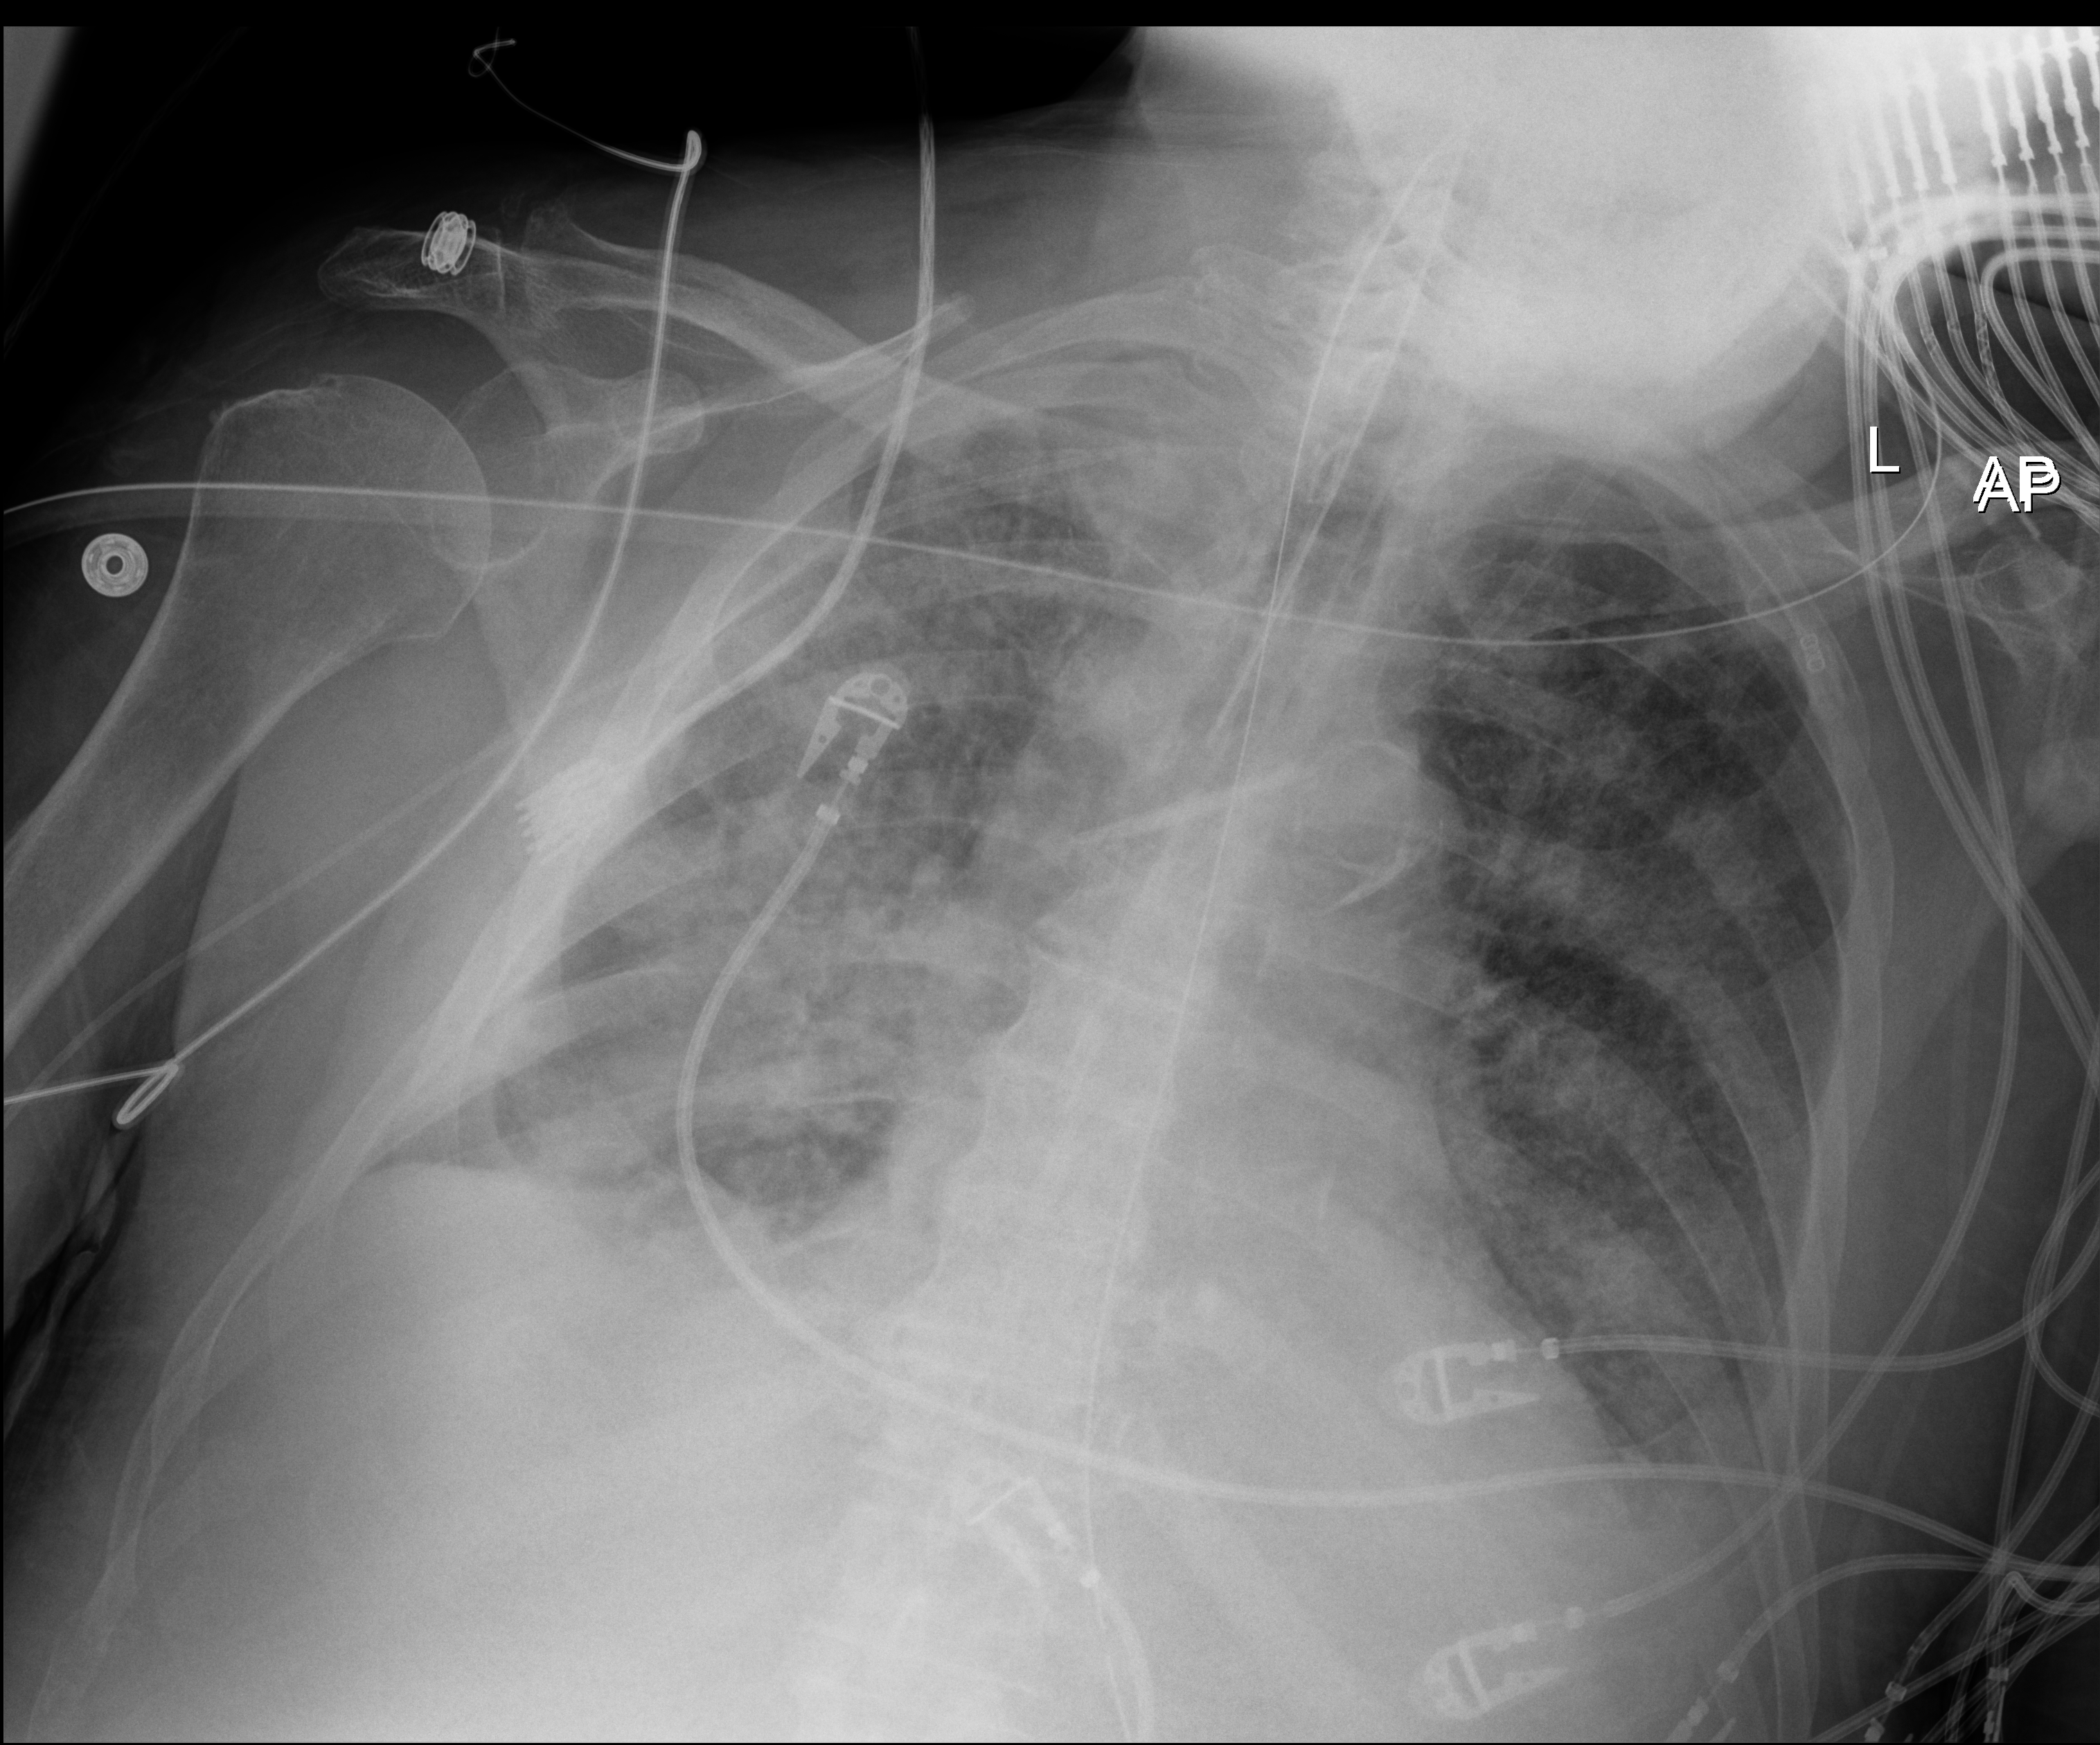
Chest X-ray (portable), anteroposterior (AP) projection. Patient hospitalised with COVID-19; male, aged 75–90 years.
From the hospital-stay record, not from the radiograph (when in the stay this image was taken is not recorded): other chronic lung disease (admission record): no; diabetes (admission record): yes.